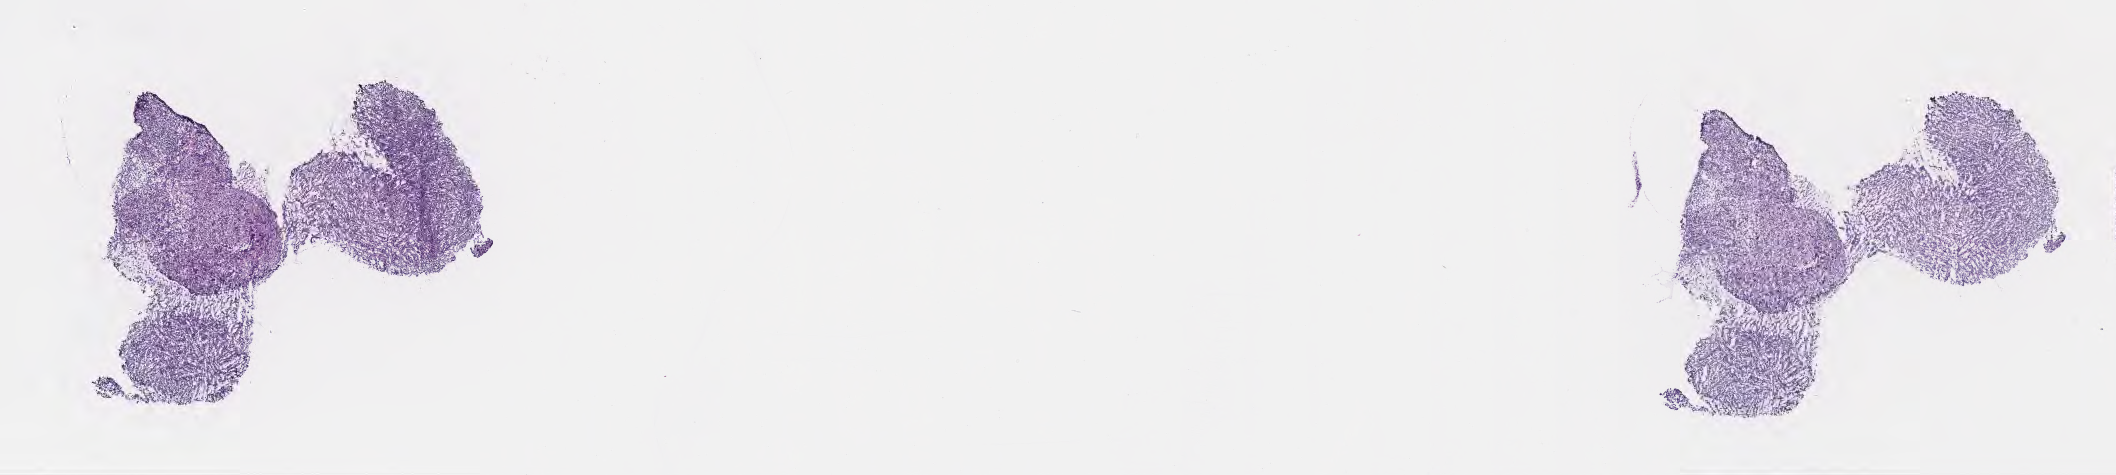
H&E whole-slide image, a low-resolution overview of the entire scanned area, about 17.1 x 3.8 mm; cryosection; primary tumor. Patient: female, age 12 years. Pathologist review of this section (percent, as recorded): tumor cells 90%, tumor nuclei 90%, stromal cells 5%, necrosis 5%, normal cells 0%. Infiltration values recorded for this section: lymphocyte infiltration 30%, monocyte infiltration 30%, neutrophil infiltration 10%.
Diagnosis: Burkitt lymphoma, NOS.